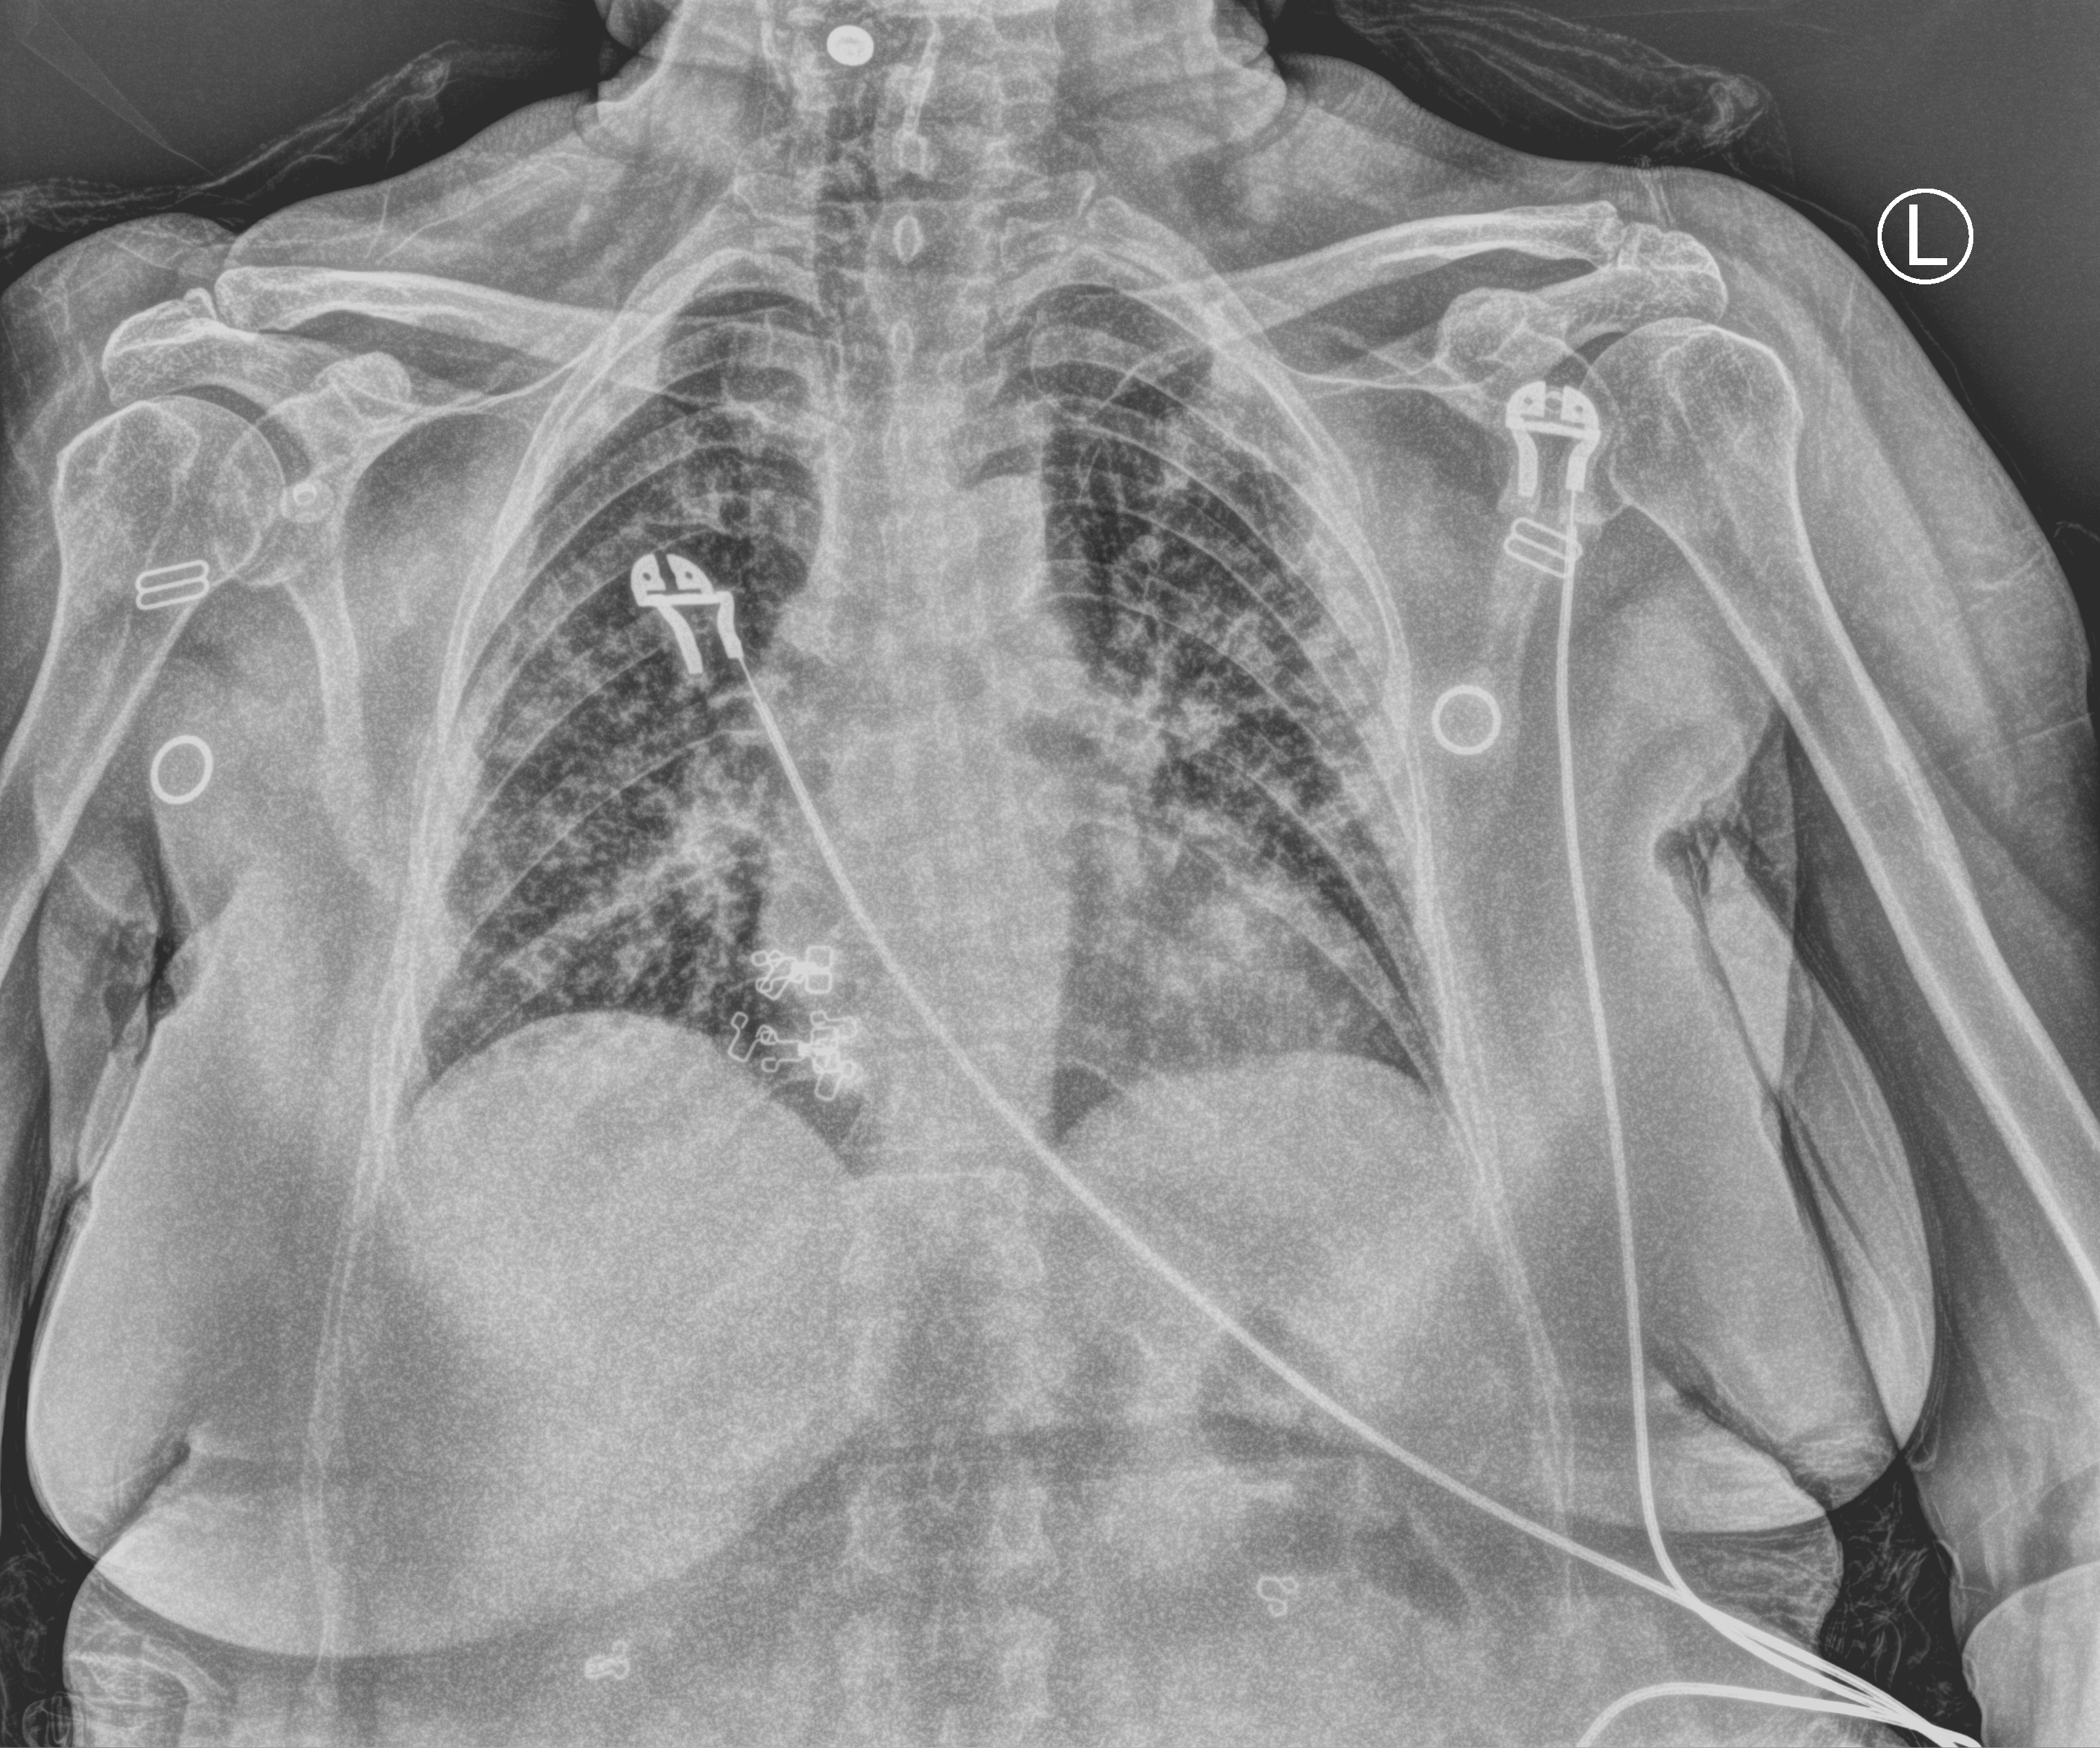
Bedside chest radiograph (computed radiography), anteroposterior (AP) projection. Female patient hospitalised with COVID-19, age 60–74 years.
From the hospital-stay record, not from the radiograph (when in the stay this image was taken is not recorded): COPD (admission record): no; mechanically ventilated during this hospital stay: no.